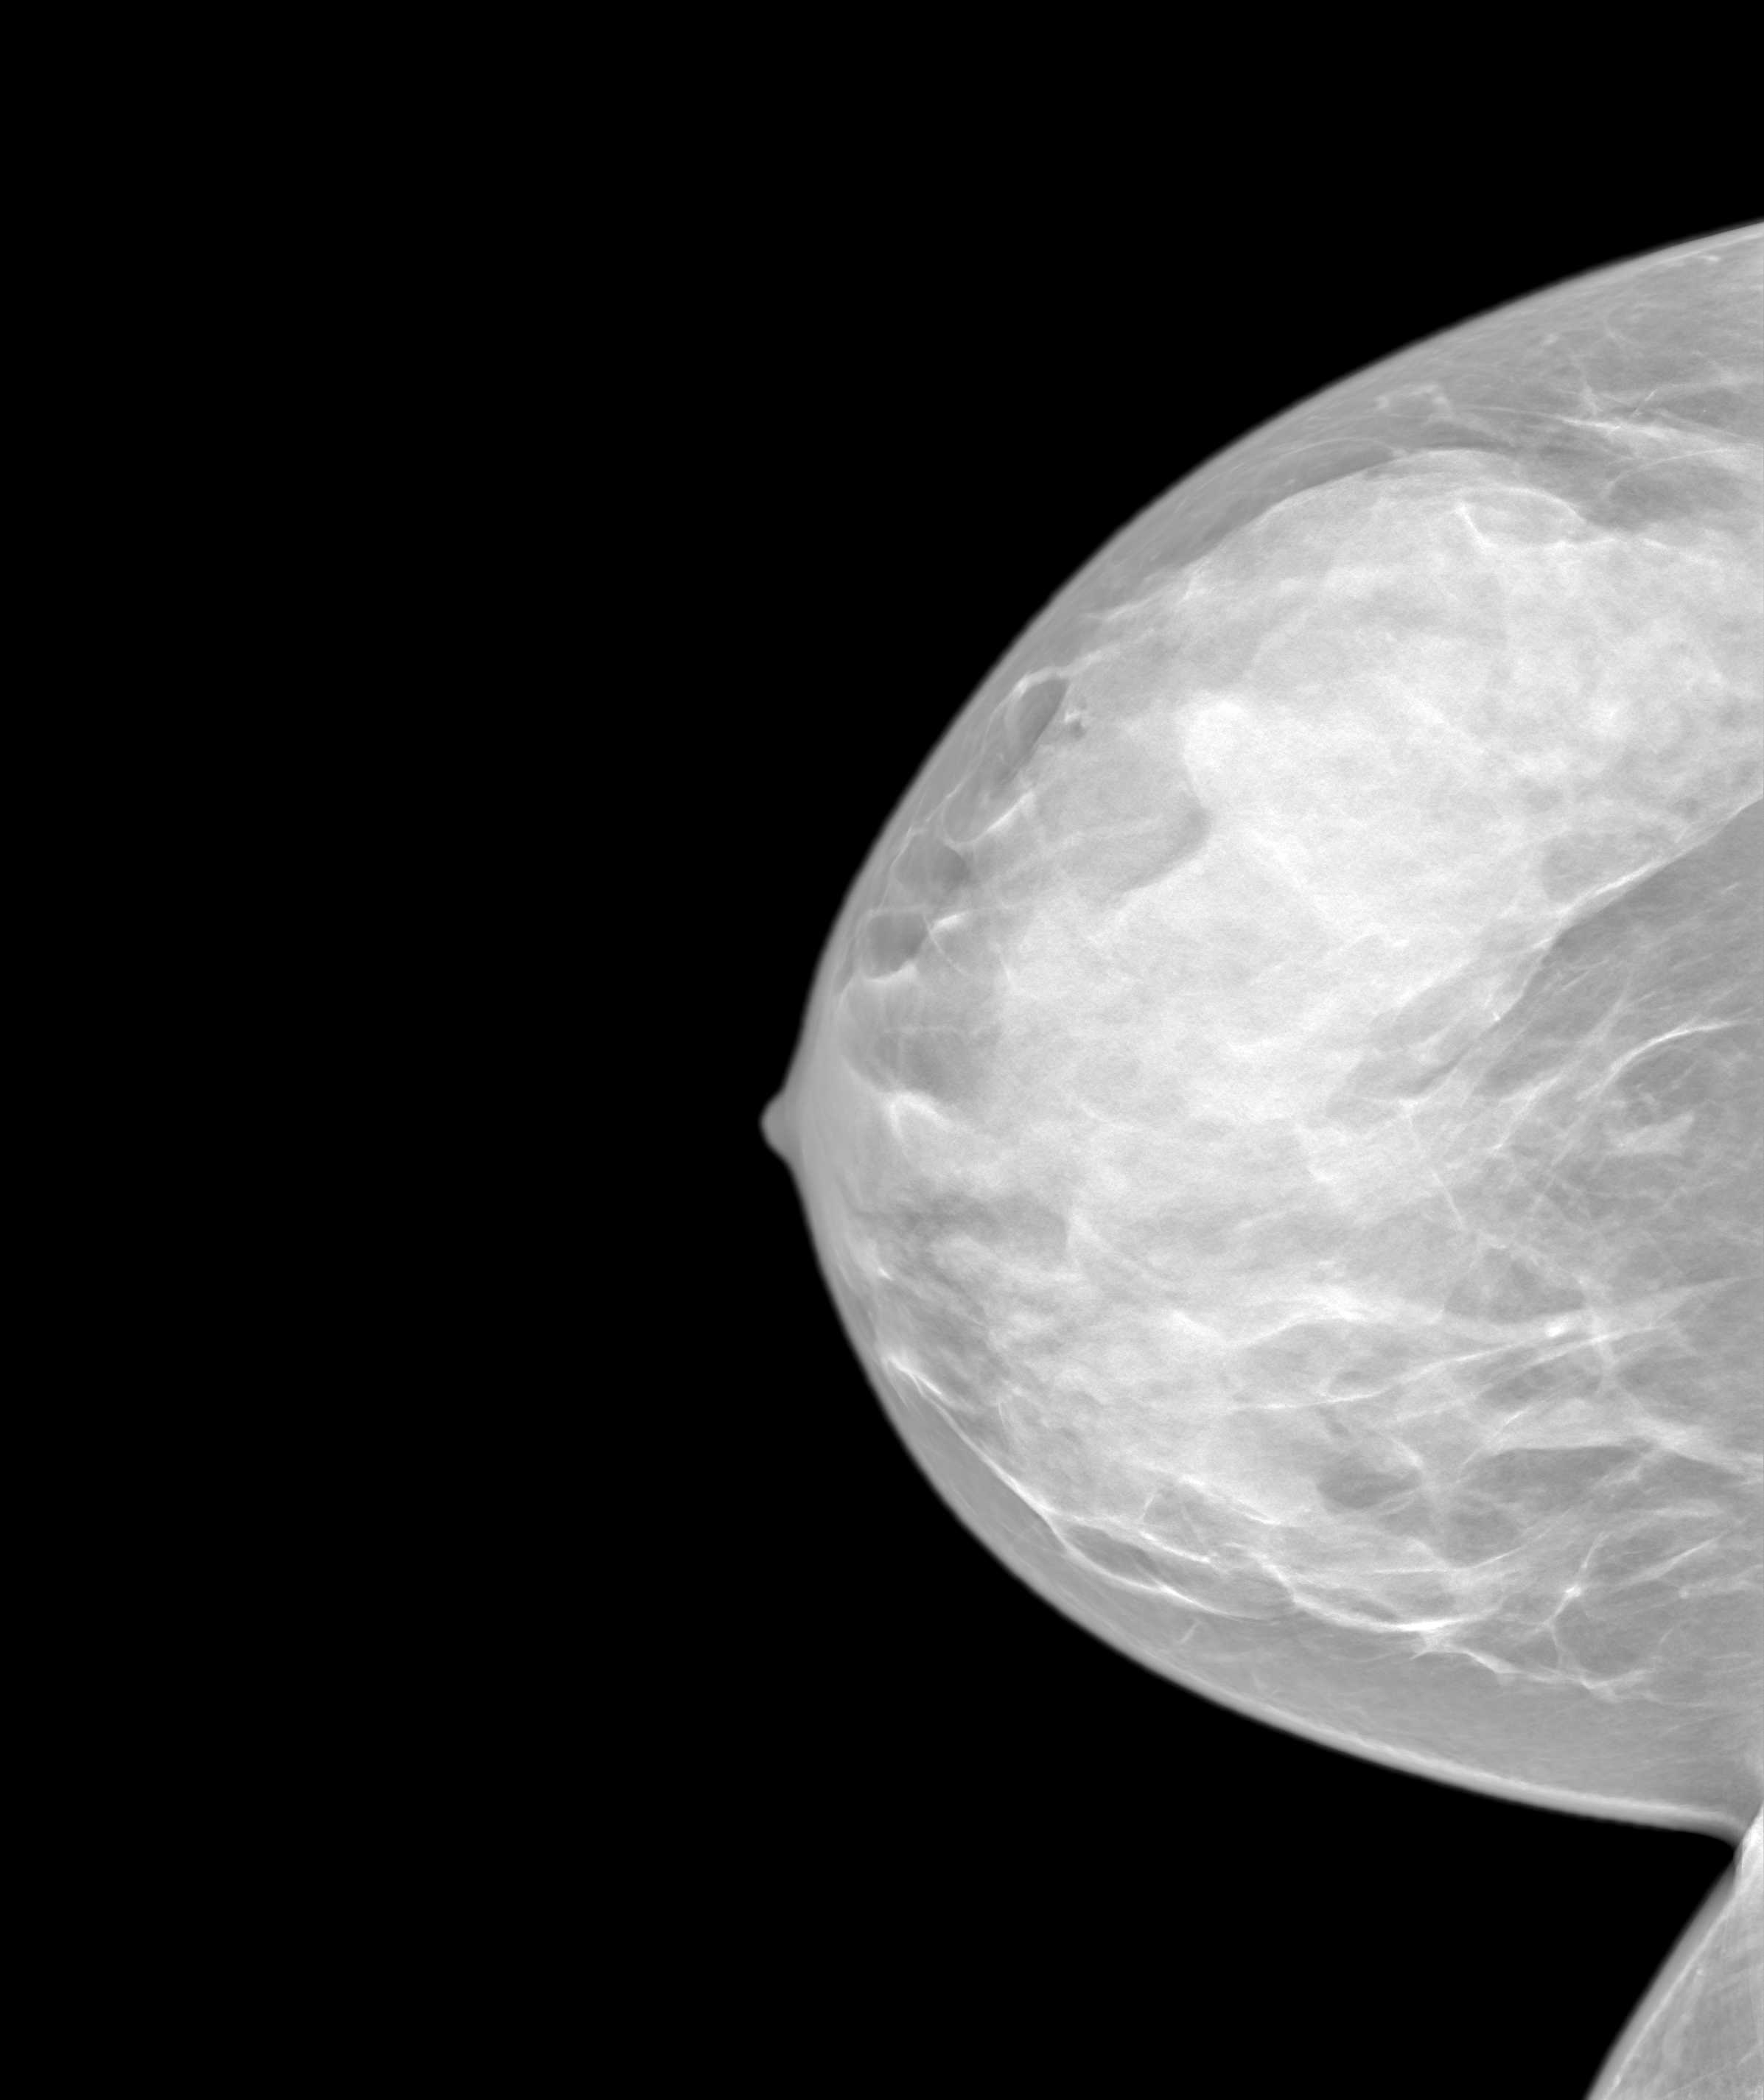
Screening examination, system: SenoIris_1SP1.1(421). Patient: female, 44 years.
Image type: synthesized 2-D view from tomosynthesis. Breast: right. Projection: CC view.